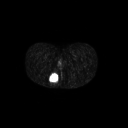
FDG PET of an extremity soft-tissue mass (from a PET/CT study), one axial slice. Position 22 of 267 along the scan axis. 3.27 mm slice thickness. 128 × 128 image matrix, field of view 700 × 700 mm. Patient: female, 17 years. Case-level facts recorded for this patient, not image findings: histological type: epithelioid sarcoma; grade: intermediate; site of the primary tumour: right buttock.
Structures marked on this image (expert contour drawn on MRI and transferred to this co-registered scan by the dataset authors):
- gross tumour volume including surrounding oedema: bounding box (x1, y1, x2, y2) in pixels: (48, 73, 60, 86)
- gross tumour volume (mass): (49, 73, 59, 83)